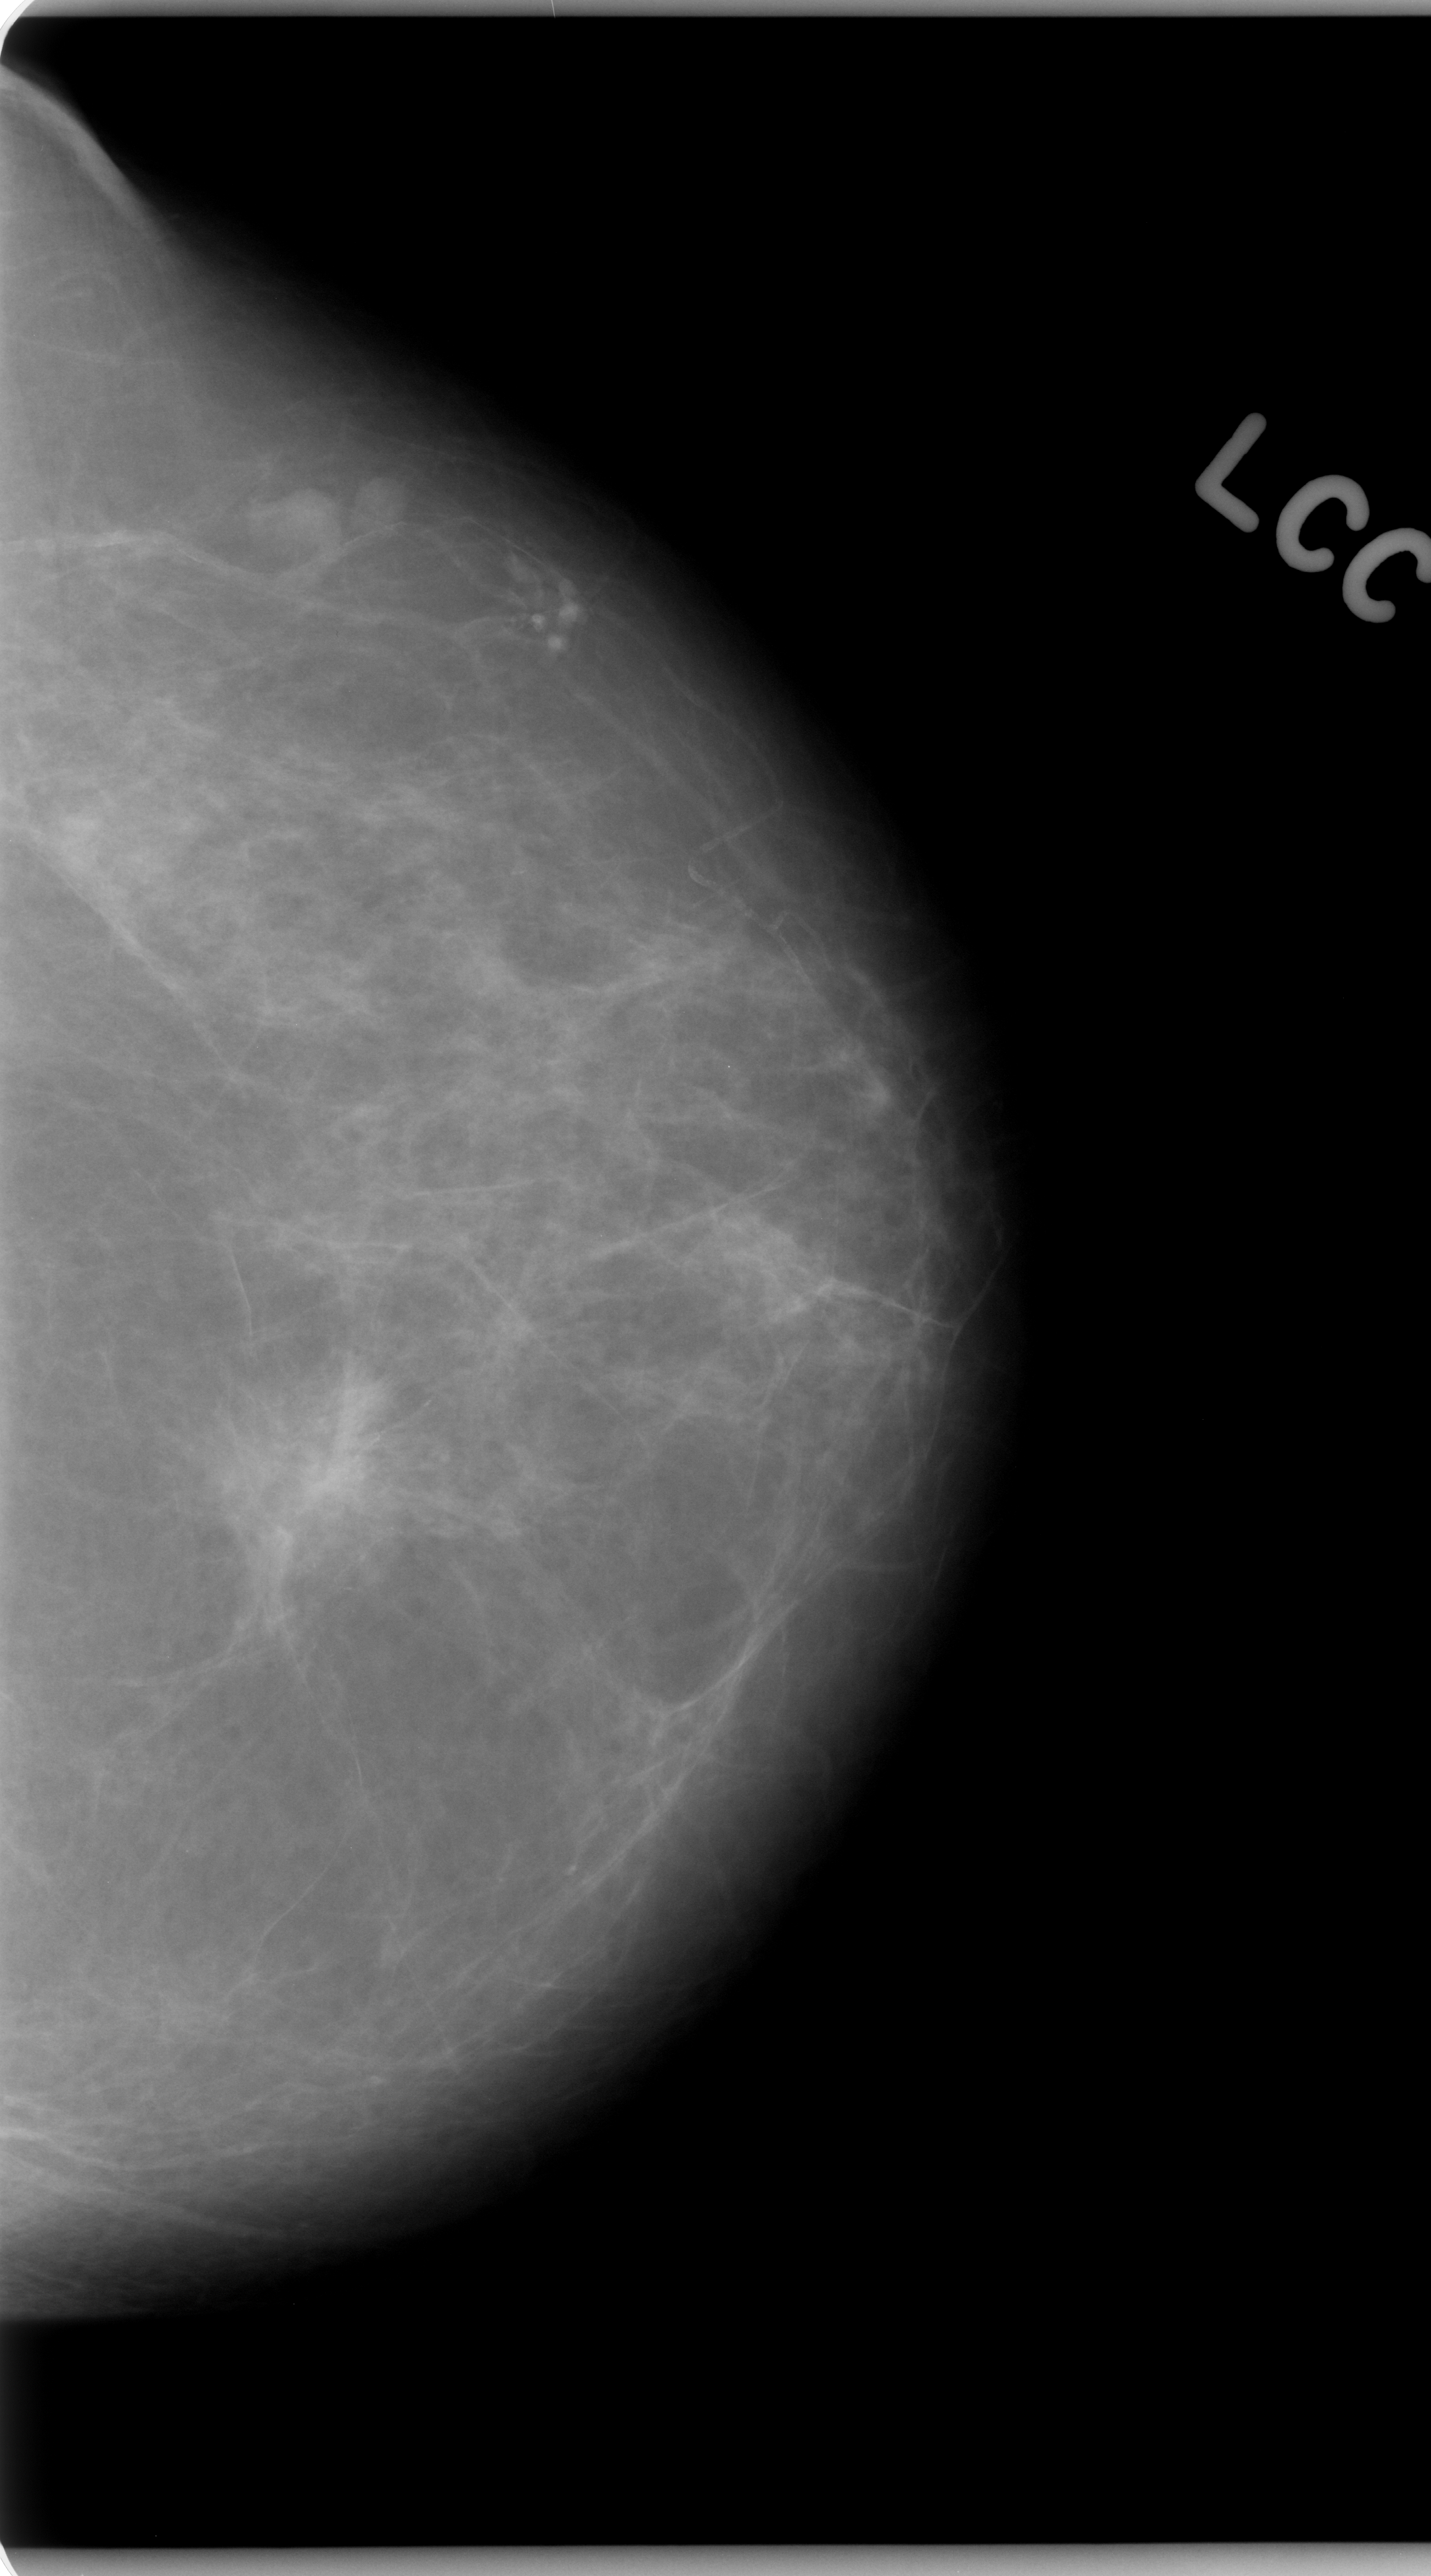
Digitized screen-film mammogram. Left breast. CC view. BI-RADS breast density category 1 (scale 1–4). 1431 × 2576 image matrix.
Expert-marked regions of interest on this film, with their recorded descriptors:
- calcifications, morphology amorphous, distribution clustered; BI-RADS assessment category 5; pathology (as recorded): malignant: bounding box [x1, y1, x2, y2] px = [96, 1241, 506, 1730]